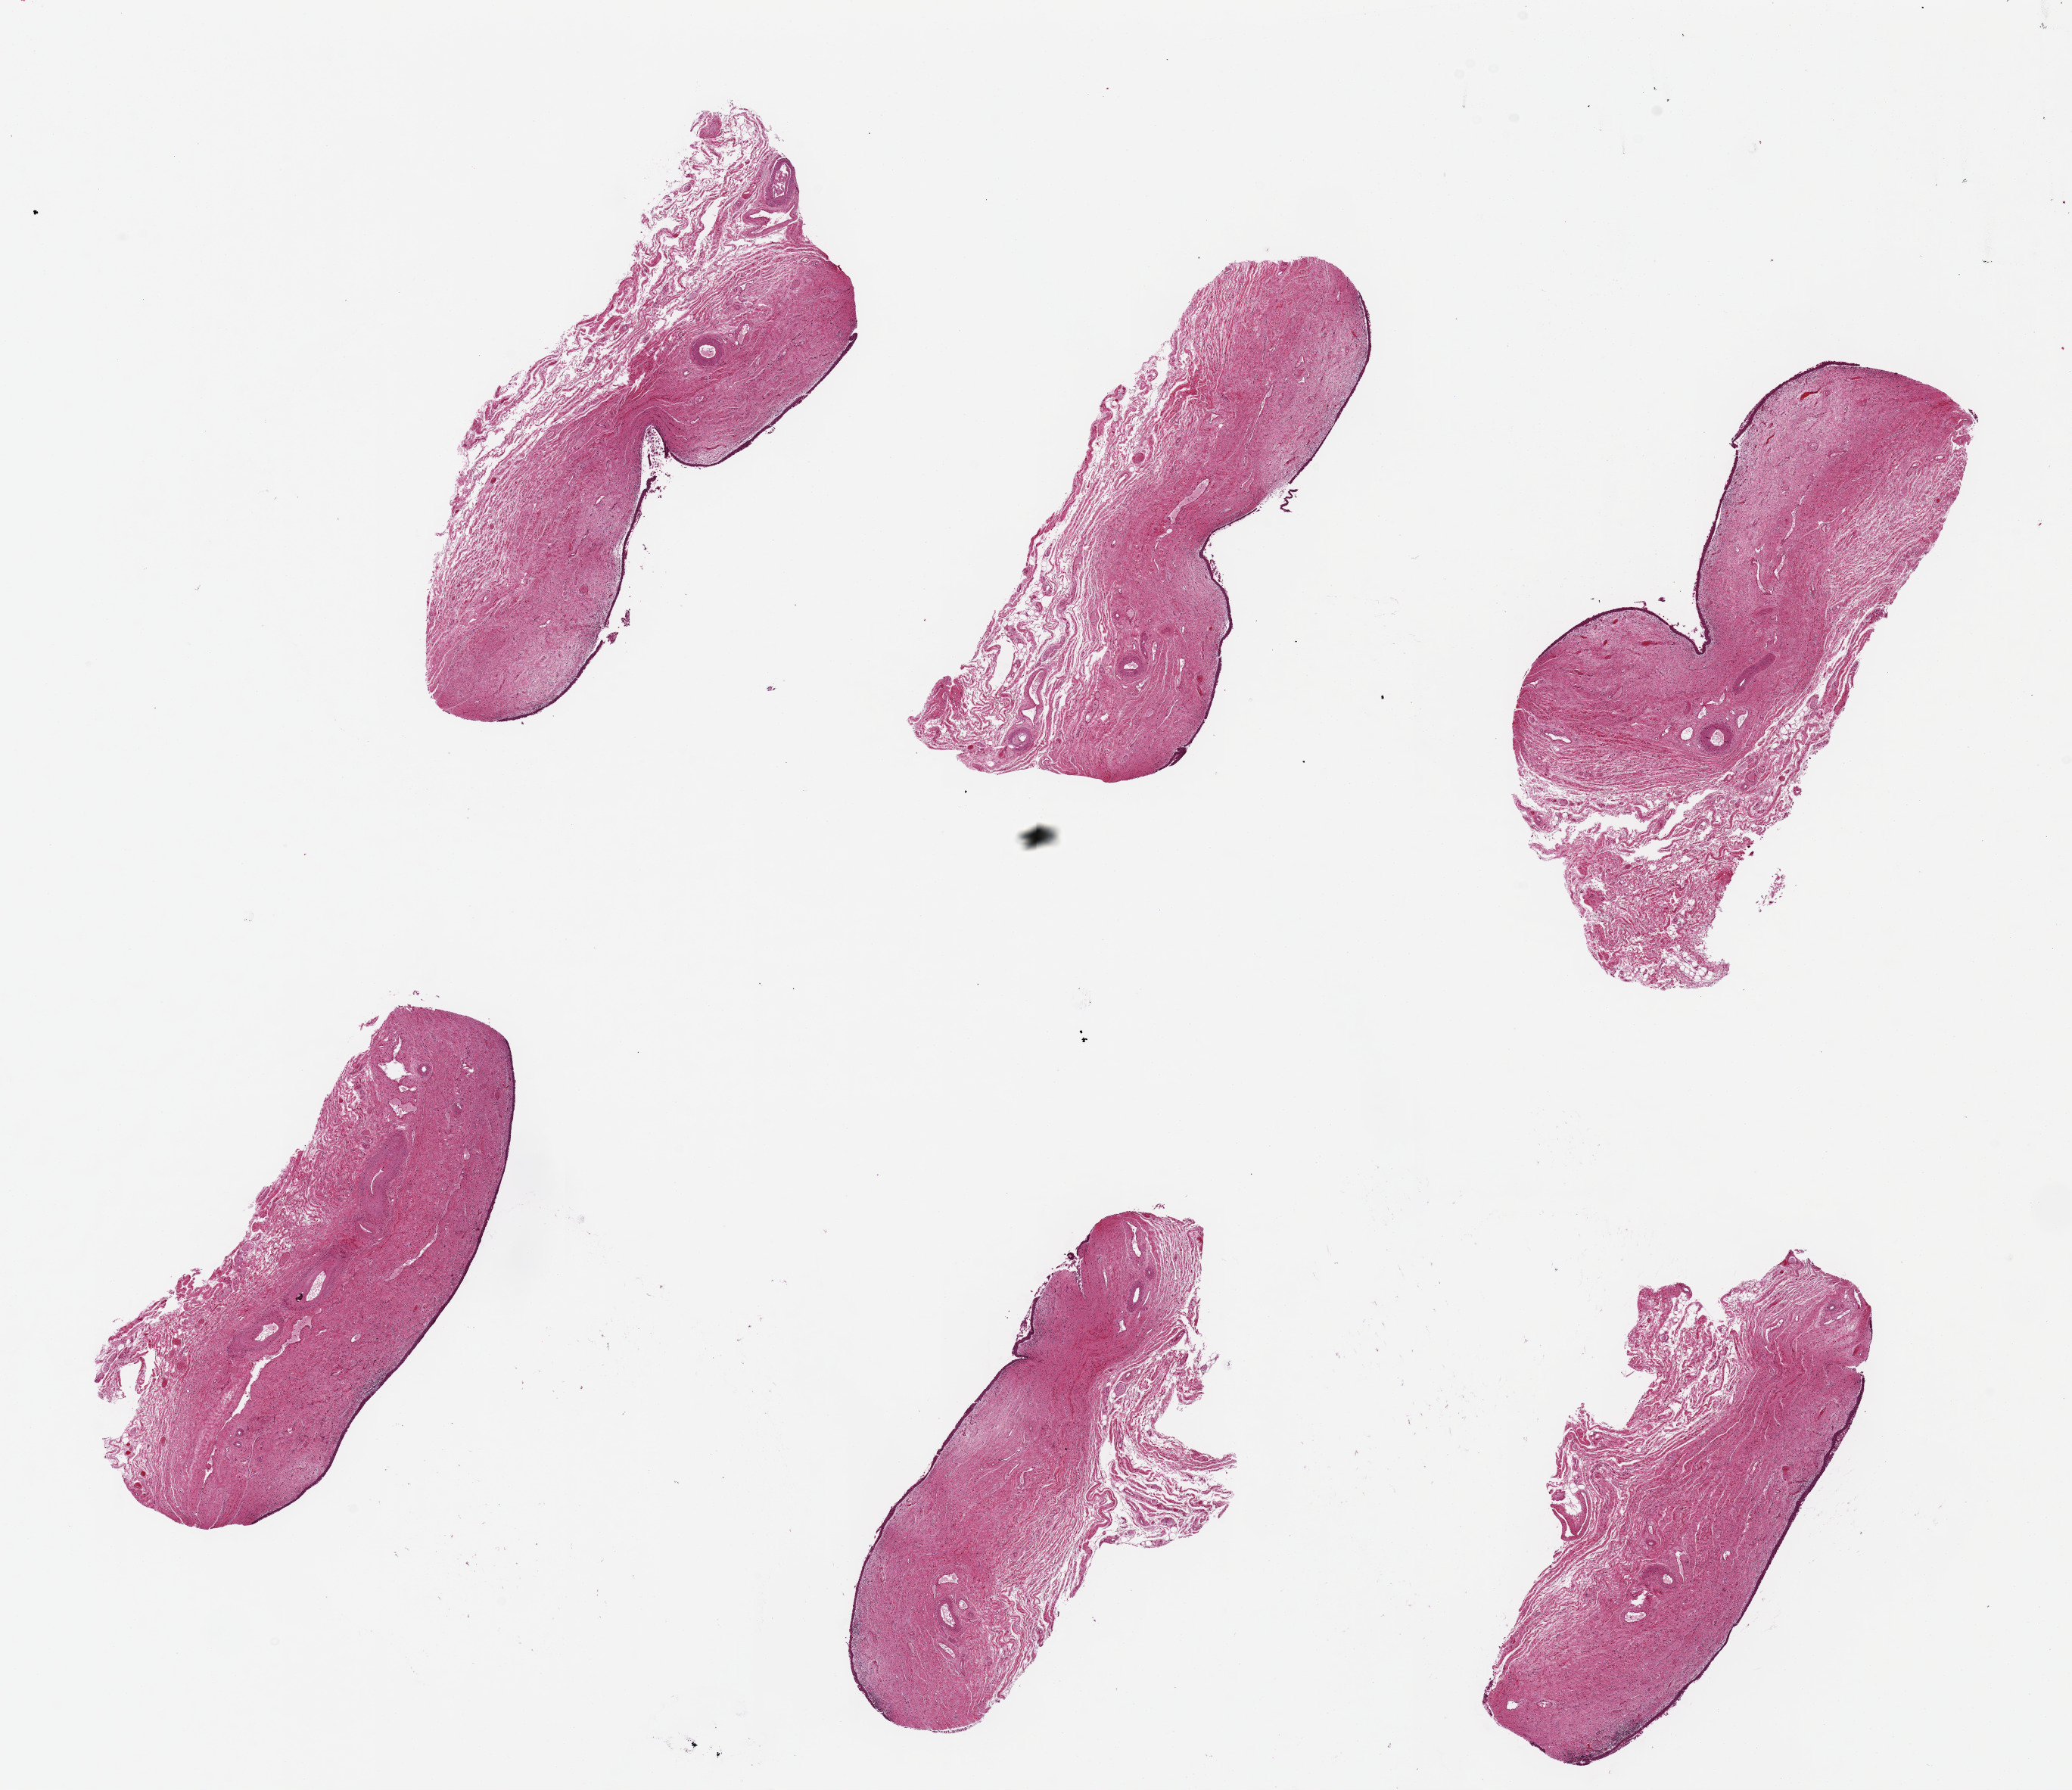
Digitized haematoxylin and eosin-stained section, a low-resolution overview of the entire scanned area, about 21.7 x 18.7 mm (slide scanned at 20x); PAXgene-fixed paraffin-embedded (PFPE) section; target tissue: vagina; tissue donor sample. Donor sex: female.
Review note (as recorded): 6 pieces up to 7x3 mm; epithelium partially sloughed.